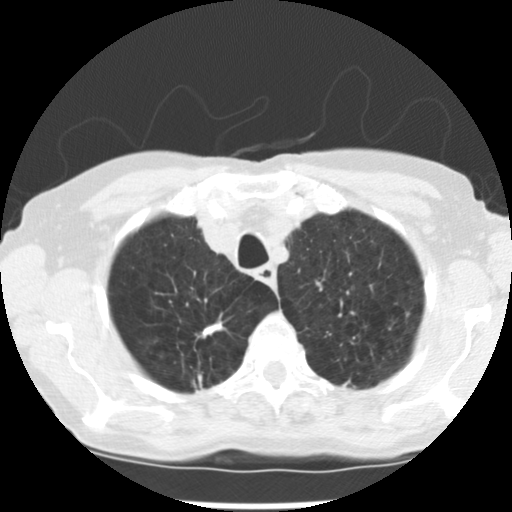
Axial slice from a low-dose chest CT screening exam. Baseline annual screen. Lung window (W 1500 / L -600 HU). Standard (soft-tissue) reconstruction kernel (STANDARD). Slice 38 of 265 in the series. 512 × 512 image matrix, field of view 300 × 300 mm. Female, age 72 years at enrolment. Current smoker at enrolment.
Expert reader's lesion annotation, box from (x=183, y=311) to (x=232, y=349) px. The screening reader recorded 3 non-calcified nodules or masses ≥4 mm on this exam; which of them this box marks is not recorded. Official screen result: positive, change unspecified: nodule(s) >= 4 mm or enlarging nodule(s), mass(es), or other non-specific abnormalities suspicious for lung cancer.